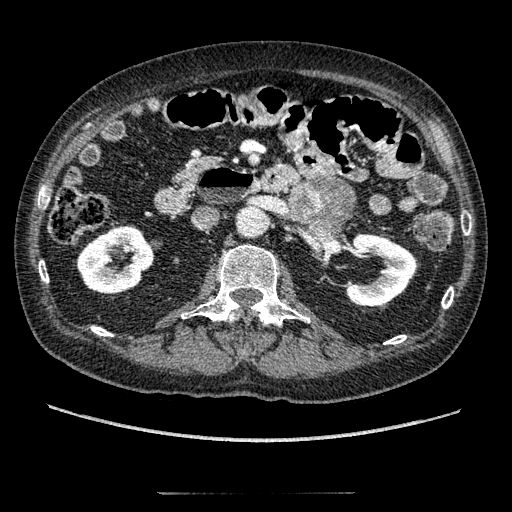
Contrast-enhanced abdominal CT, one axial slice. Slice 89 of 274 in the series (ordered by position). Reconstruction kernel STANDARD. Soft-tissue window (W 400 / L 40 HU). 1.25 mm slice thickness. 512 × 512 image matrix. Male patient, age 69 years. Case-level facts recorded for this patient, not image findings: diagnosis: adrenocortical carcinoma; tumour side: left adrenal; tumour size at pathology: 6.1 cm; Ki-67 index: 10 %; stage (as recorded): 3.
Outlined on this slice (semi-automatic segmentation, software-assisted and operator-edited):
- mass: bounding box <293,180,354,227> (left, top, right, bottom; pixels)